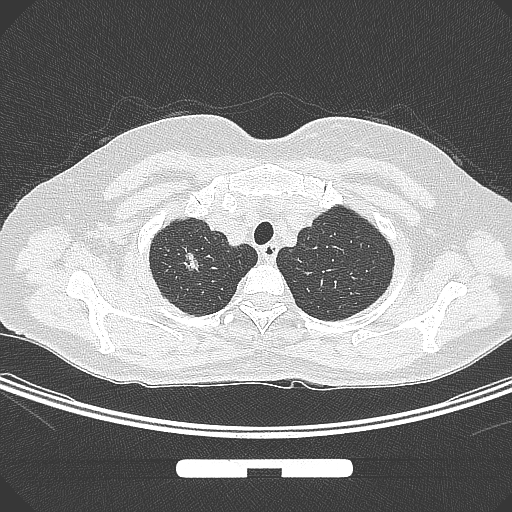
Chest CT, one axial slice. Position 257 of 295 along the scan axis. Lung window (W 1500 / L -600 HU). 512 × 512 image matrix. Patient: female, 58 years. Case-level facts recorded for this patient, not image findings: clinical TNM (as recorded): T1b N0 M0.
Structures marked on this image (rectangle marked by the reading radiologist):
- lung tumour (recorded histology: adenocarcinoma): bounding box <171,244,201,279> (left, top, right, bottom; pixels)